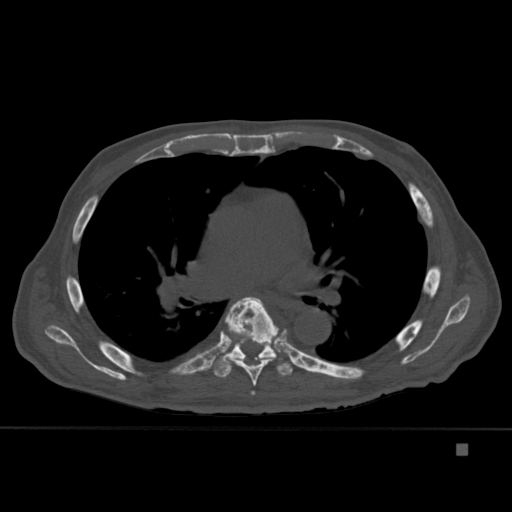
CT including the spine, one axial slice; slice 288 of 451 in the series (ordered by position); bone window (W 1800 / L 400 HU); 1.5 mm slice thickness; 512 × 512 image matrix, field of view 378 × 378 mm. Patient: male, 75 years. Case-level facts recorded for this patient, not image findings: primary cancer: prostate.
Structures marked on this image (semi-automatic segmentation, software-assisted and operator-edited):
- T5 vertebra: bounding box <251,391,255,395> (left, top, right, bottom; pixels)
- T6 vertebra: <223,297,279,386>
- T7 vertebra: <209,337,295,378>